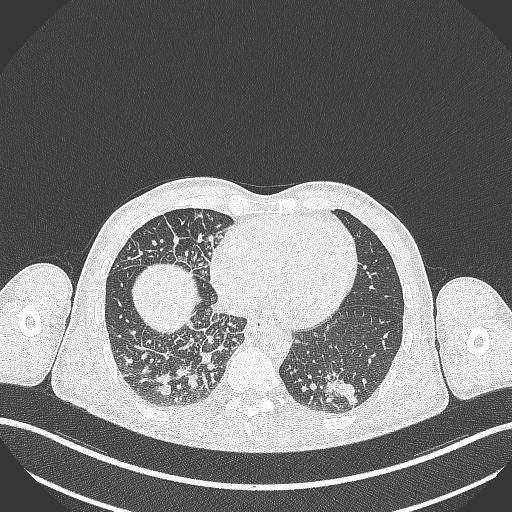
Chest CT, one axial slice. Position 94 of 348 along the scan axis. Reconstruction kernel B70f. Lung window (W 1500 / L -600 HU). 512 × 512 image matrix, field of view 400 × 400 mm. Male patient, age 49 years. Case-level facts recorded for this patient, not image findings: clinical TNM (as recorded): T2b N1 M0.
Structures marked on this image (rectangle marked by the reading radiologist):
- lung tumour (recorded histology: adenocarcinoma): box from (x=315, y=366) to (x=362, y=408) px